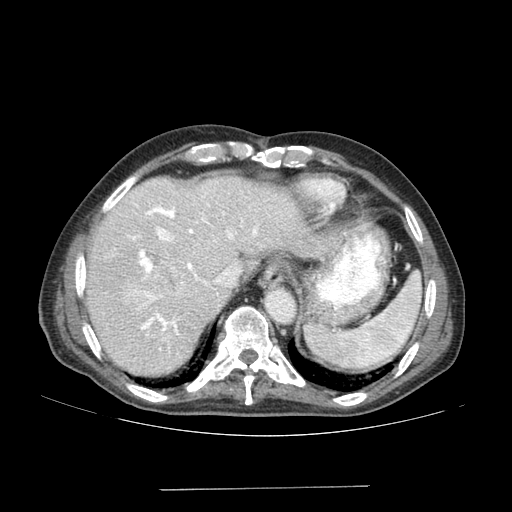
Contrast-enhanced abdominal CT (liver protocol), one axial slice; slice 132 of 192 in the series (ordered by position); 120 kVp; soft-tissue window (W 400 / L 40 HU); 512 × 512 image matrix. Case-level facts recorded for this patient, not image findings: diagnosis: hepatocellular carcinoma (patient treated with transarterial chemoembolisation; whether this scan precedes or follows treatment is not stated here); TNM stage (as recorded): Stage-IVA; Child-Pugh class: A; tumour nodularity: uninodular.
Annotated regions visible in this slice (semi-automatic segmentation, software-assisted and operator-edited):
- liver parenchyma outside the tumour (the mass and vessels are separate outlines, so this box may not span the whole liver): box from (x=86, y=176) to (x=326, y=376) px
- mass: (x=123, y=269)–(x=173, y=307)
- liver vessels: (x=128, y=196)–(x=258, y=350)